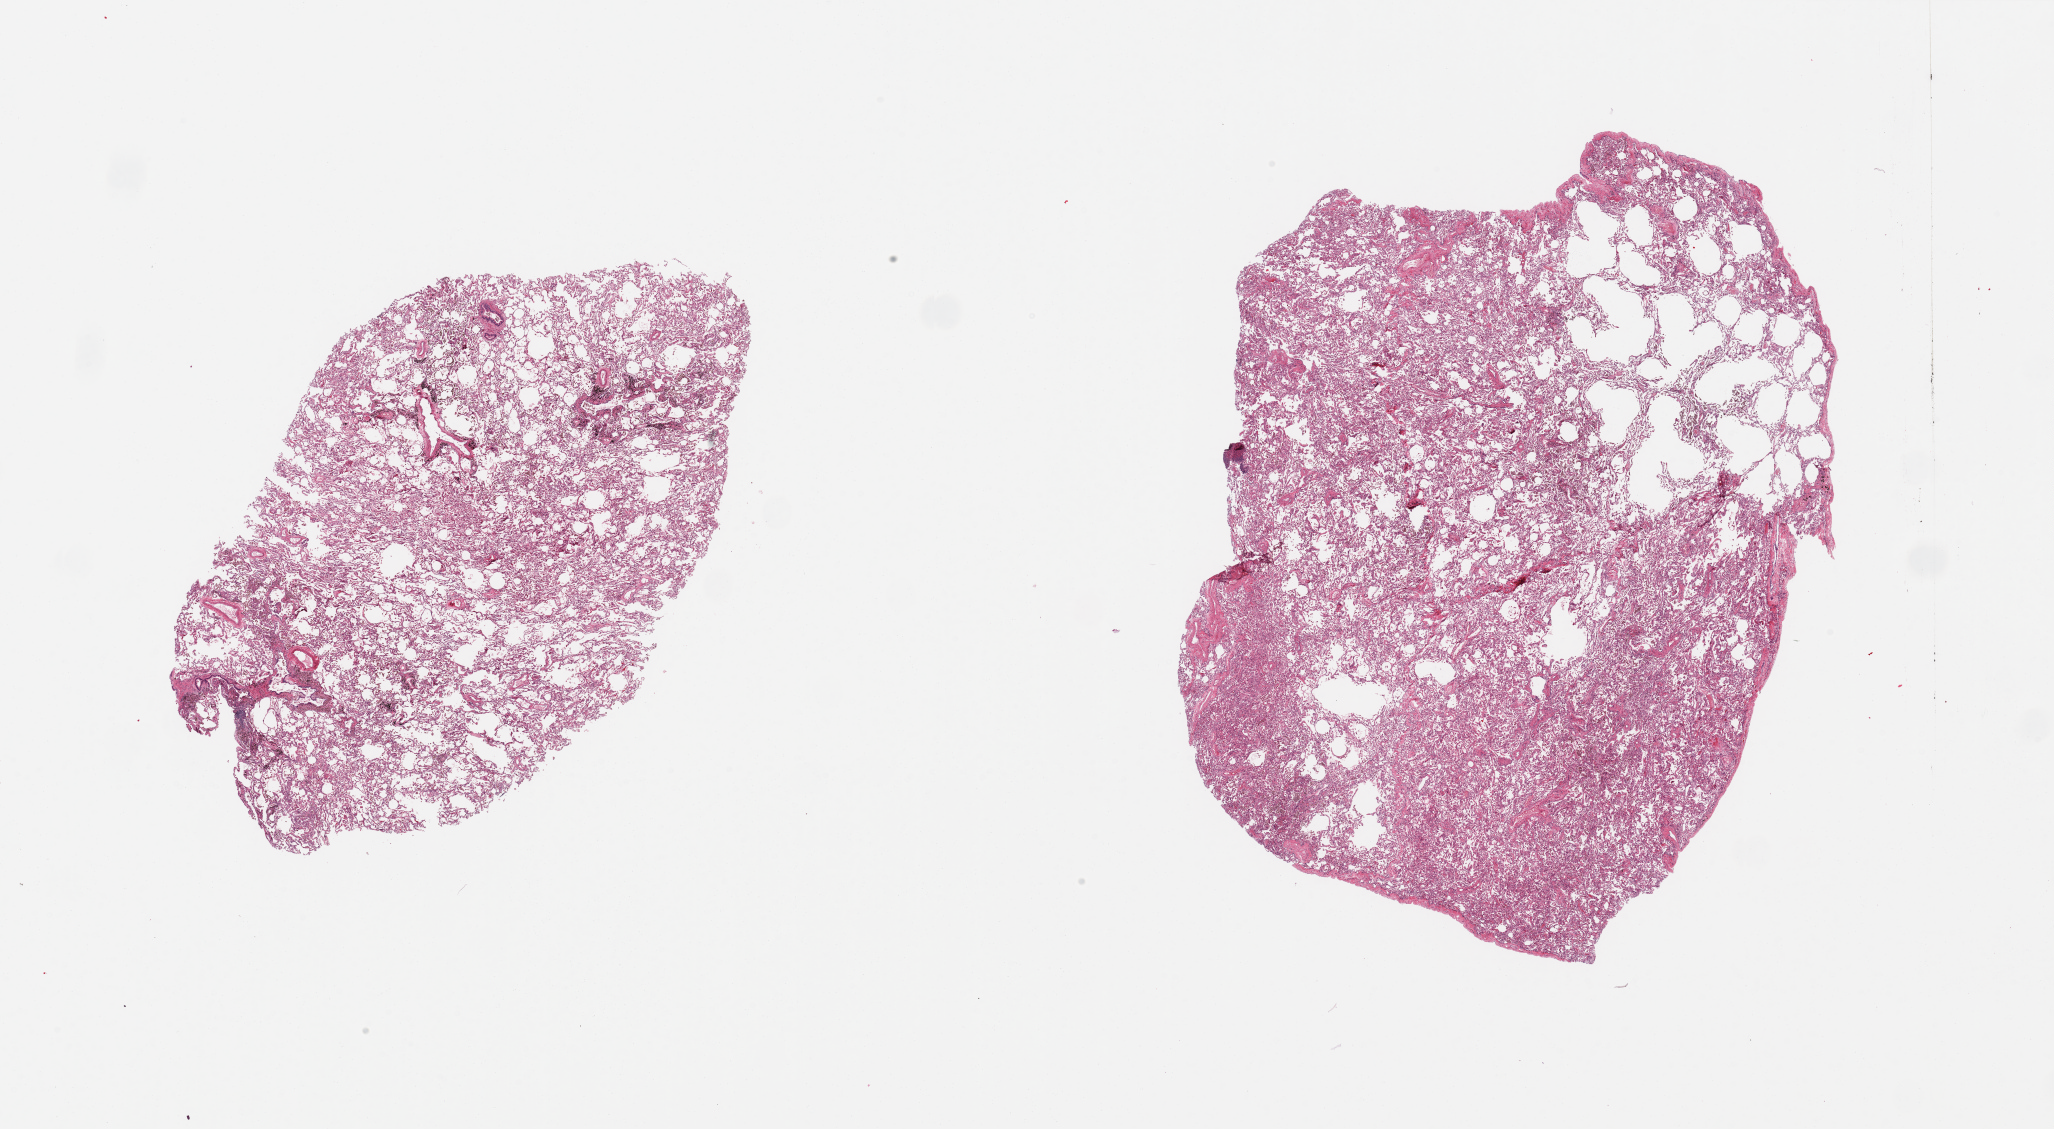
Digitized H&E-stained section, brightfield — whole scanned area (about 32.5 x 17.9 mm) shown as a low-resolution overview. PAXgene-fixed paraffin-embedded (PFPE) section. Target tissue: lung. Tissue donor sample. Donor sex: female.
Pathologist's review note for this sample: 2 pieces; pigmented macrophages in alveoli and lymphoid nodules; no fibrosis; delicate alveolar walls.